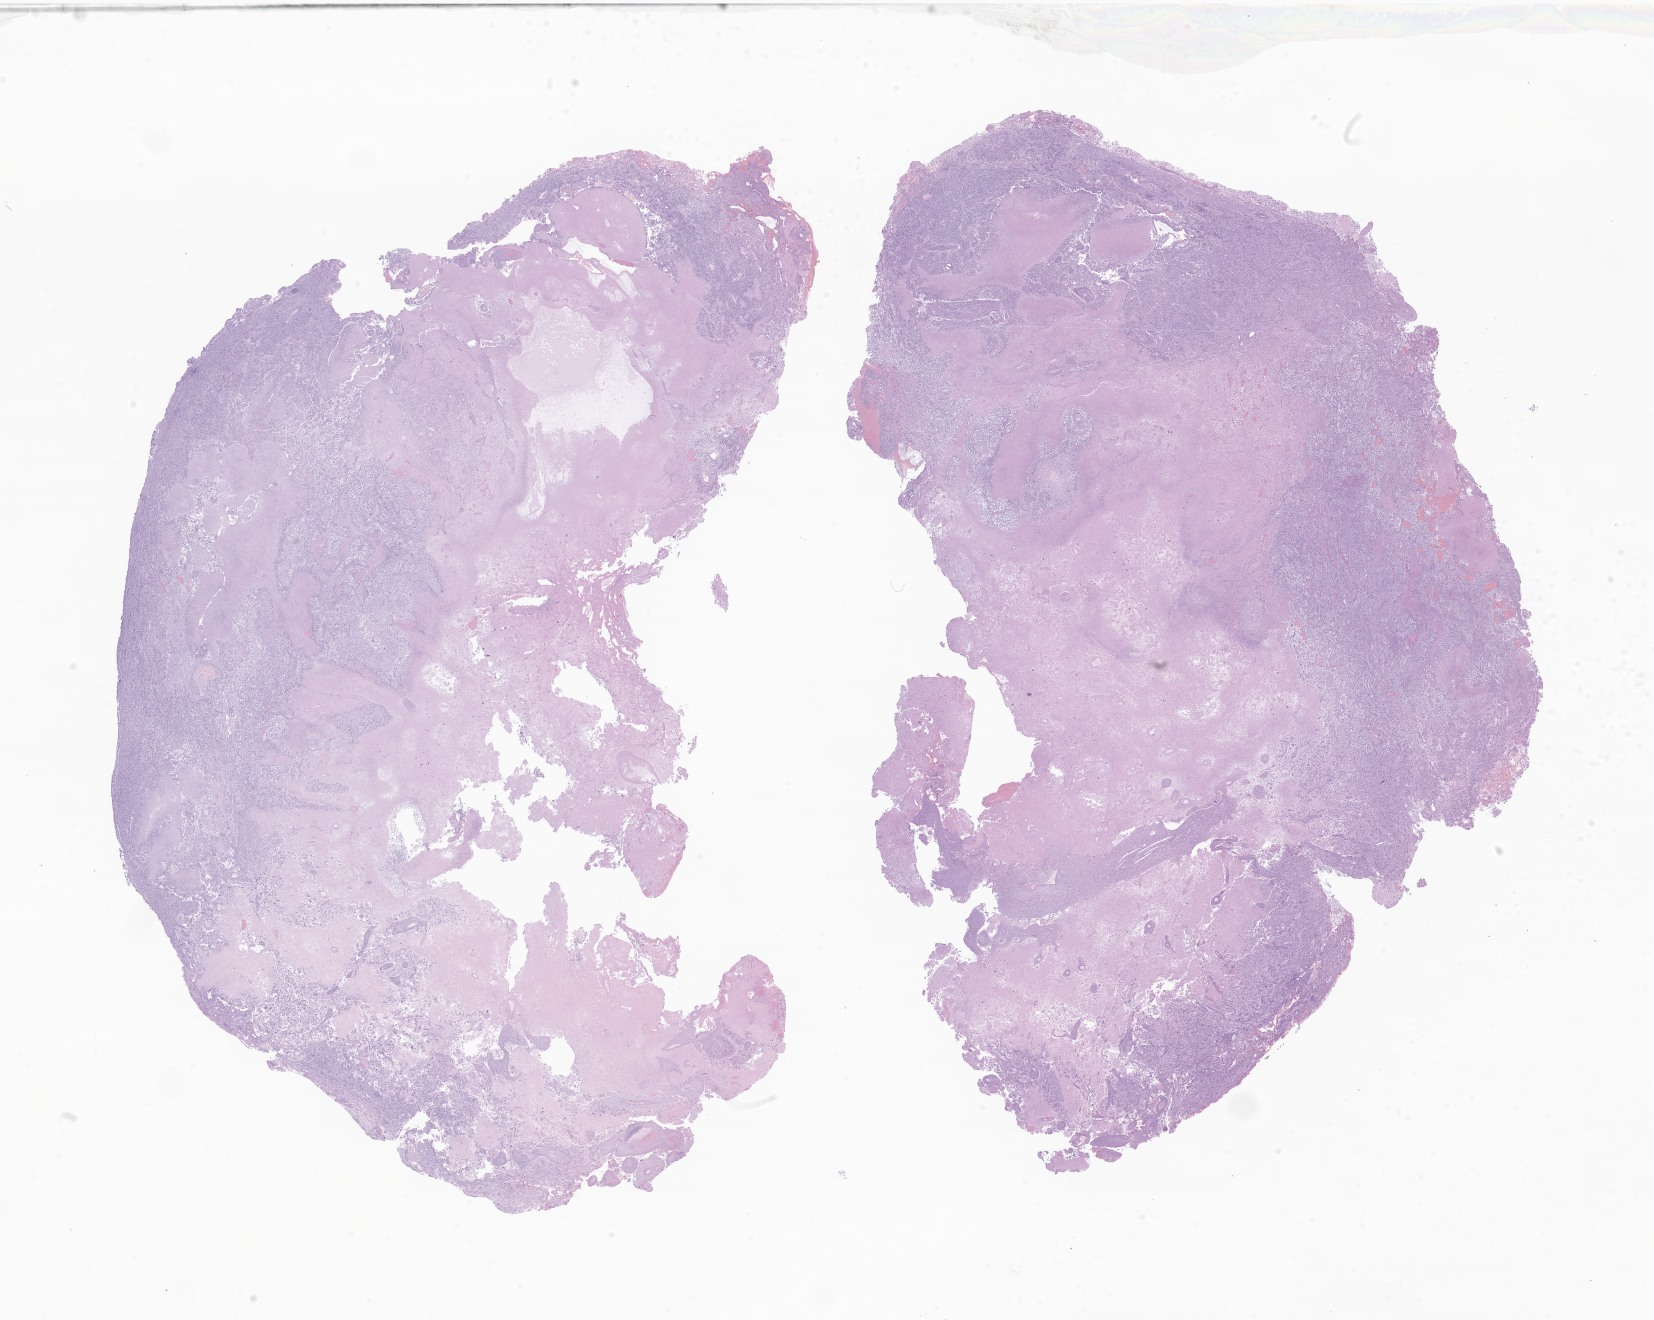
Whole-slide image, haematoxylin and eosin stain of tumor tissue from the brain, a low-resolution overview of the entire scanned area, about 27.9 x 22.3 mm. Formalin-fixed, paraffin-embedded (FFPE) tissue. Patient: male, age 97 months (8 years 1 month).
Recorded diagnosis: Glioma, malignant.